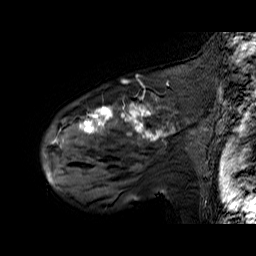
Breast MRI (dynamic contrast-enhanced), one sagittal slice; position 47 of 60 along the scan axis; dynamic contrast-enhanced series, time point 2 of 6 at this slice position (early post-contrast); 1.5 T; TE 6.3 ms, TR 32.9 ms; 4 mm slice thickness; 256 × 256 image matrix, field of view 200 × 200 mm. Female patient. From the clinical record (not read from this slice): setting: breast cancer imaged before/during neoadjuvant chemotherapy; receptor status: HER2-positive.
Outlined on this slice (semi-automatic segmentation, software-assisted and operator-edited):
- analysis volume of interest (the breast-tissue region the enhancement analysis was run in; not a lesion): box from (x=48, y=92) to (x=195, y=174) px
- tumour enhancement mask (voxels above the 100 % enhancement threshold inside the analysis volume of interest): (x=52, y=102)–(x=174, y=145)